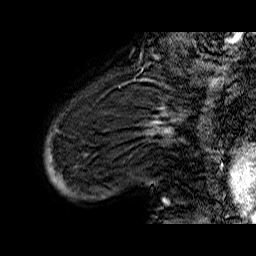
Breast MRI (dynamic contrast-enhanced), one sagittal slice. Dynamic contrast-enhanced series, time point 2 of 6 at this slice position (early post-contrast). 1.5 T. TE 6.5 ms, TR 32.9 ms. 4 mm slice thickness. 256 × 256 image matrix, field of view 200 × 200 mm. Female patient. From the clinical record (not read from this slice): setting: breast cancer imaged before/during neoadjuvant chemotherapy; receptor status: HR-positive, HER2-negative.
Structures marked on this image (semi-automatically segmented with operator editing):
- analysis volume of interest (the breast-tissue region the enhancement analysis was run in; not a lesion): bounding box (x1, y1, x2, y2) in pixels: (44, 74, 176, 210)
- tumour enhancement mask (voxels above the 100 % enhancement threshold inside the analysis volume of interest): (156, 123, 169, 206)